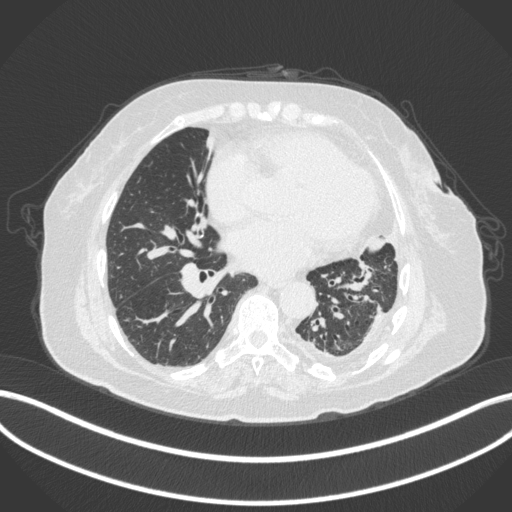
Chest CT, one axial slice. Slice 161 of 399 in the series (ordered by position). Reconstruction kernel B31f. Lung window (W 1500 / L -600 HU). 1 mm slice thickness. 512 × 512 image matrix, field of view 400 × 400 mm. Patient: female, 75 years. From the clinical record (not read from this slice): clinical TNM (as recorded): T3 N3 M1.
Outlined on this slice (bounding box drawn by a radiologist):
- lung tumour (recorded histology: adenocarcinoma): bounding box (x1, y1, x2, y2) in pixels: (364, 230, 386, 261)